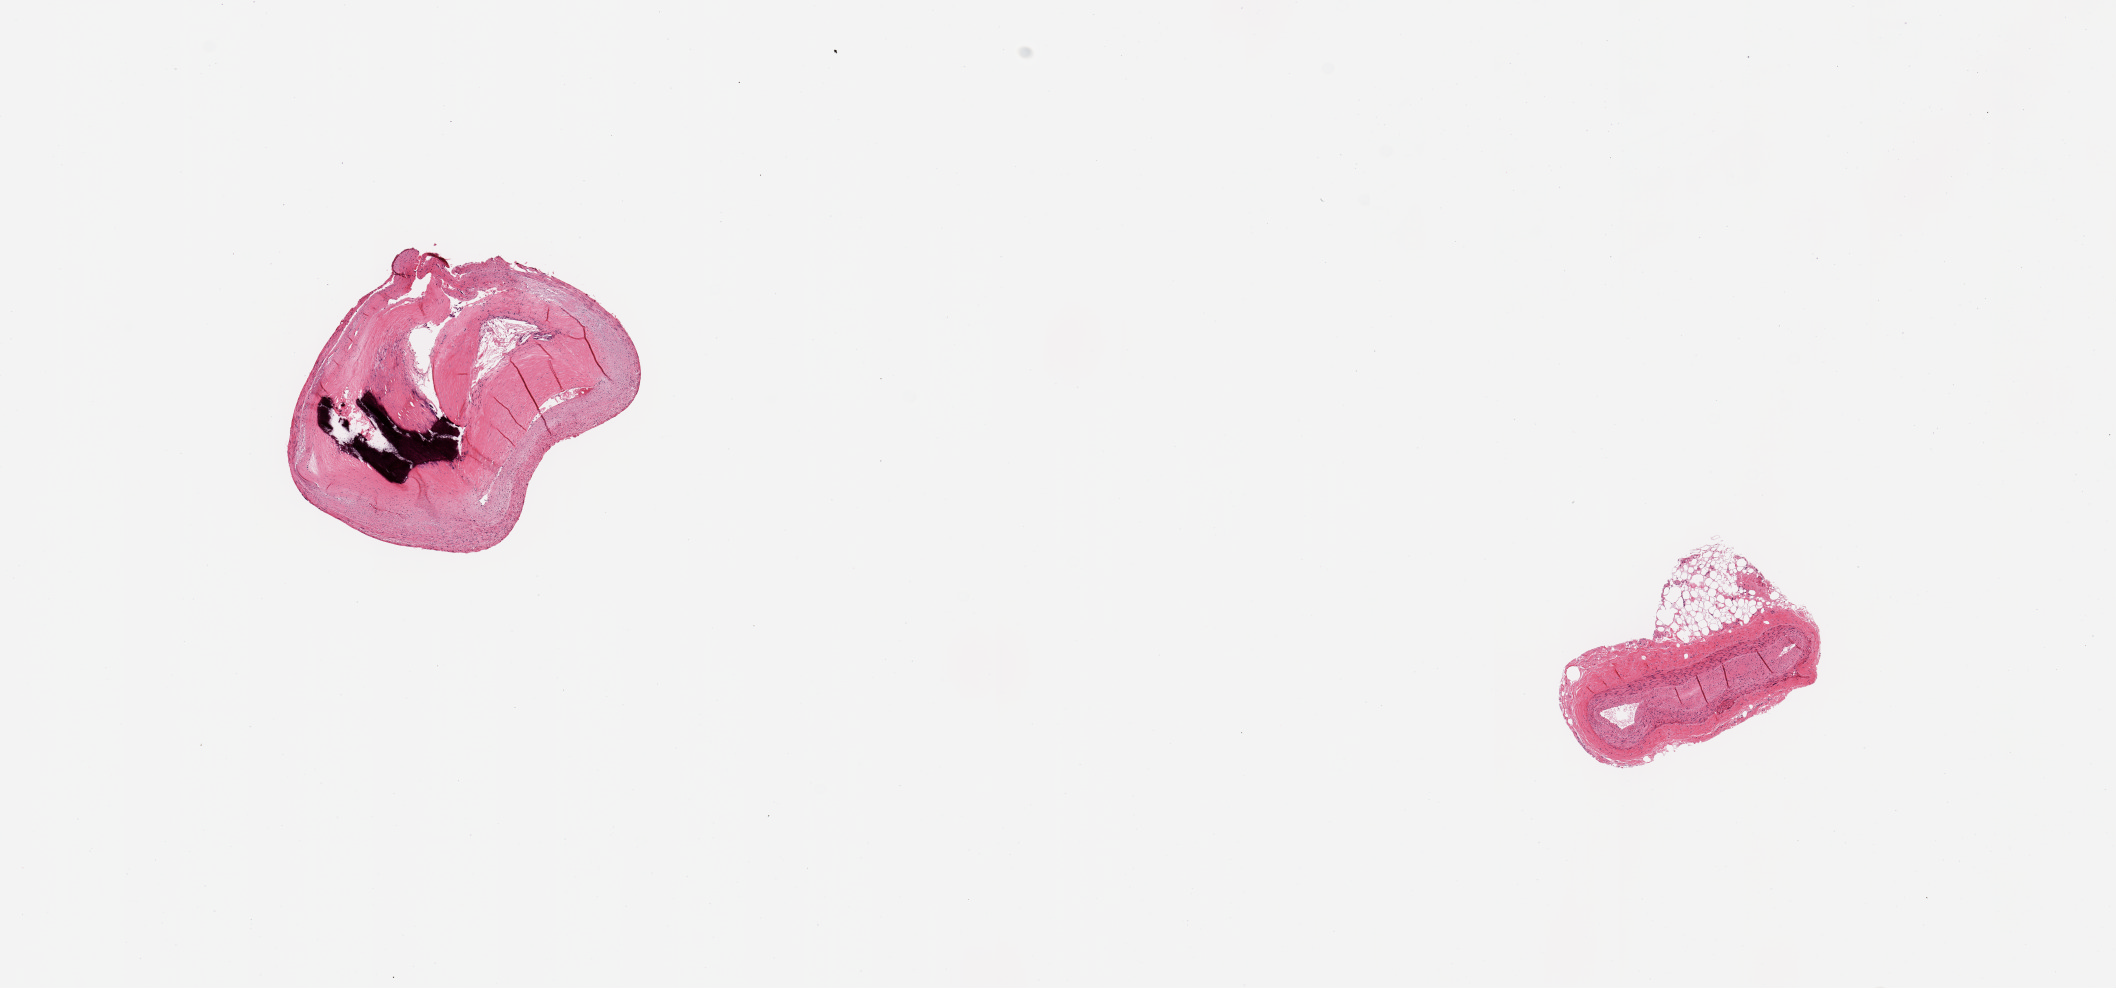
H&E whole-slide image, a low-resolution overview of the entire scanned area, about 16.7 x 7.8 mm (slide scanned at 20x), PAXgene-fixed paraffin-embedded (PFPE) section, sampled site (target tissue): coronary artery, donor tissue sample.
Reviewer comment on this tissue sample: 2 pieces; large calcified atheromatous plaque in larger piece; smaller piece has 0.6 mm external fat collection.